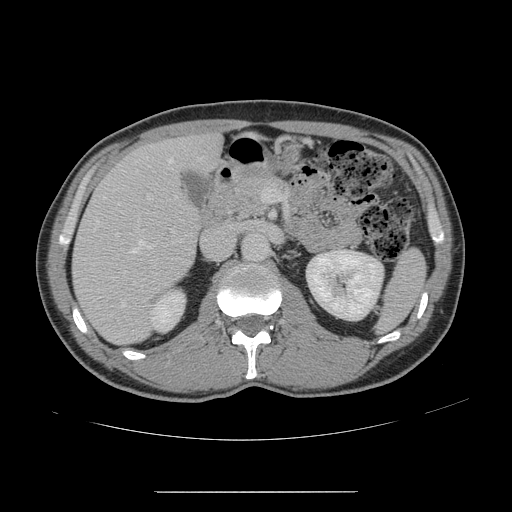
Contrast-enhanced abdominal CT, one axial slice. Position 77 of 178 along the scan axis. 120 kVp. Intravenous contrast given. Soft-tissue window (W 400 / L 40 HU). 2.5 mm slice thickness. 512 × 512 image matrix, field of view 401 × 401 mm. Male patient, age 53 years. Case-level facts recorded for this patient, not image findings: diagnosis: colorectal cancer liver metastases, imaged before liver resection; multiple liver metastases: yes; largest metastasis: 2.4 cm; chemotherapy before resection: yes.
Structures marked on this image (manually delineated by an expert):
- hepatic veins: bounding box (x1, y1, x2, y2) in pixels: (96, 159, 172, 308)
- liver: (73, 135, 221, 344)
- planned liver remnant (the part of the liver to remain after resection): (169, 135, 221, 168)
- portal vein (with intrahepatic branches): (147, 188, 267, 203)